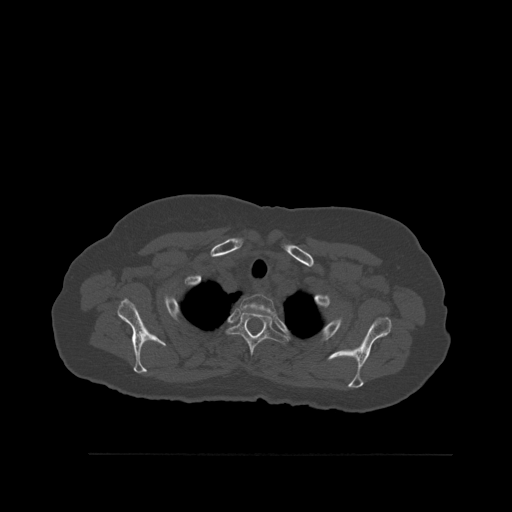
CT including the spine, one axial slice; slice 434 of 527 in the series (ordered by position); bone window (W 1800 / L 400 HU); 1.5 mm slice thickness; 512 × 512 image matrix, field of view 470 × 470 mm. Female patient, age 73 years. From the clinical record (not read from this slice): primary cancer: breast; vertebrae with lytic lesions (as recorded): L2.
Outlined on this slice (semi-automatic segmentation, software-assisted and operator-edited):
- T1 vertebra: bounding box <240,294,276,316> (left, top, right, bottom; pixels)
- T2 vertebra: <227,309,289,358>